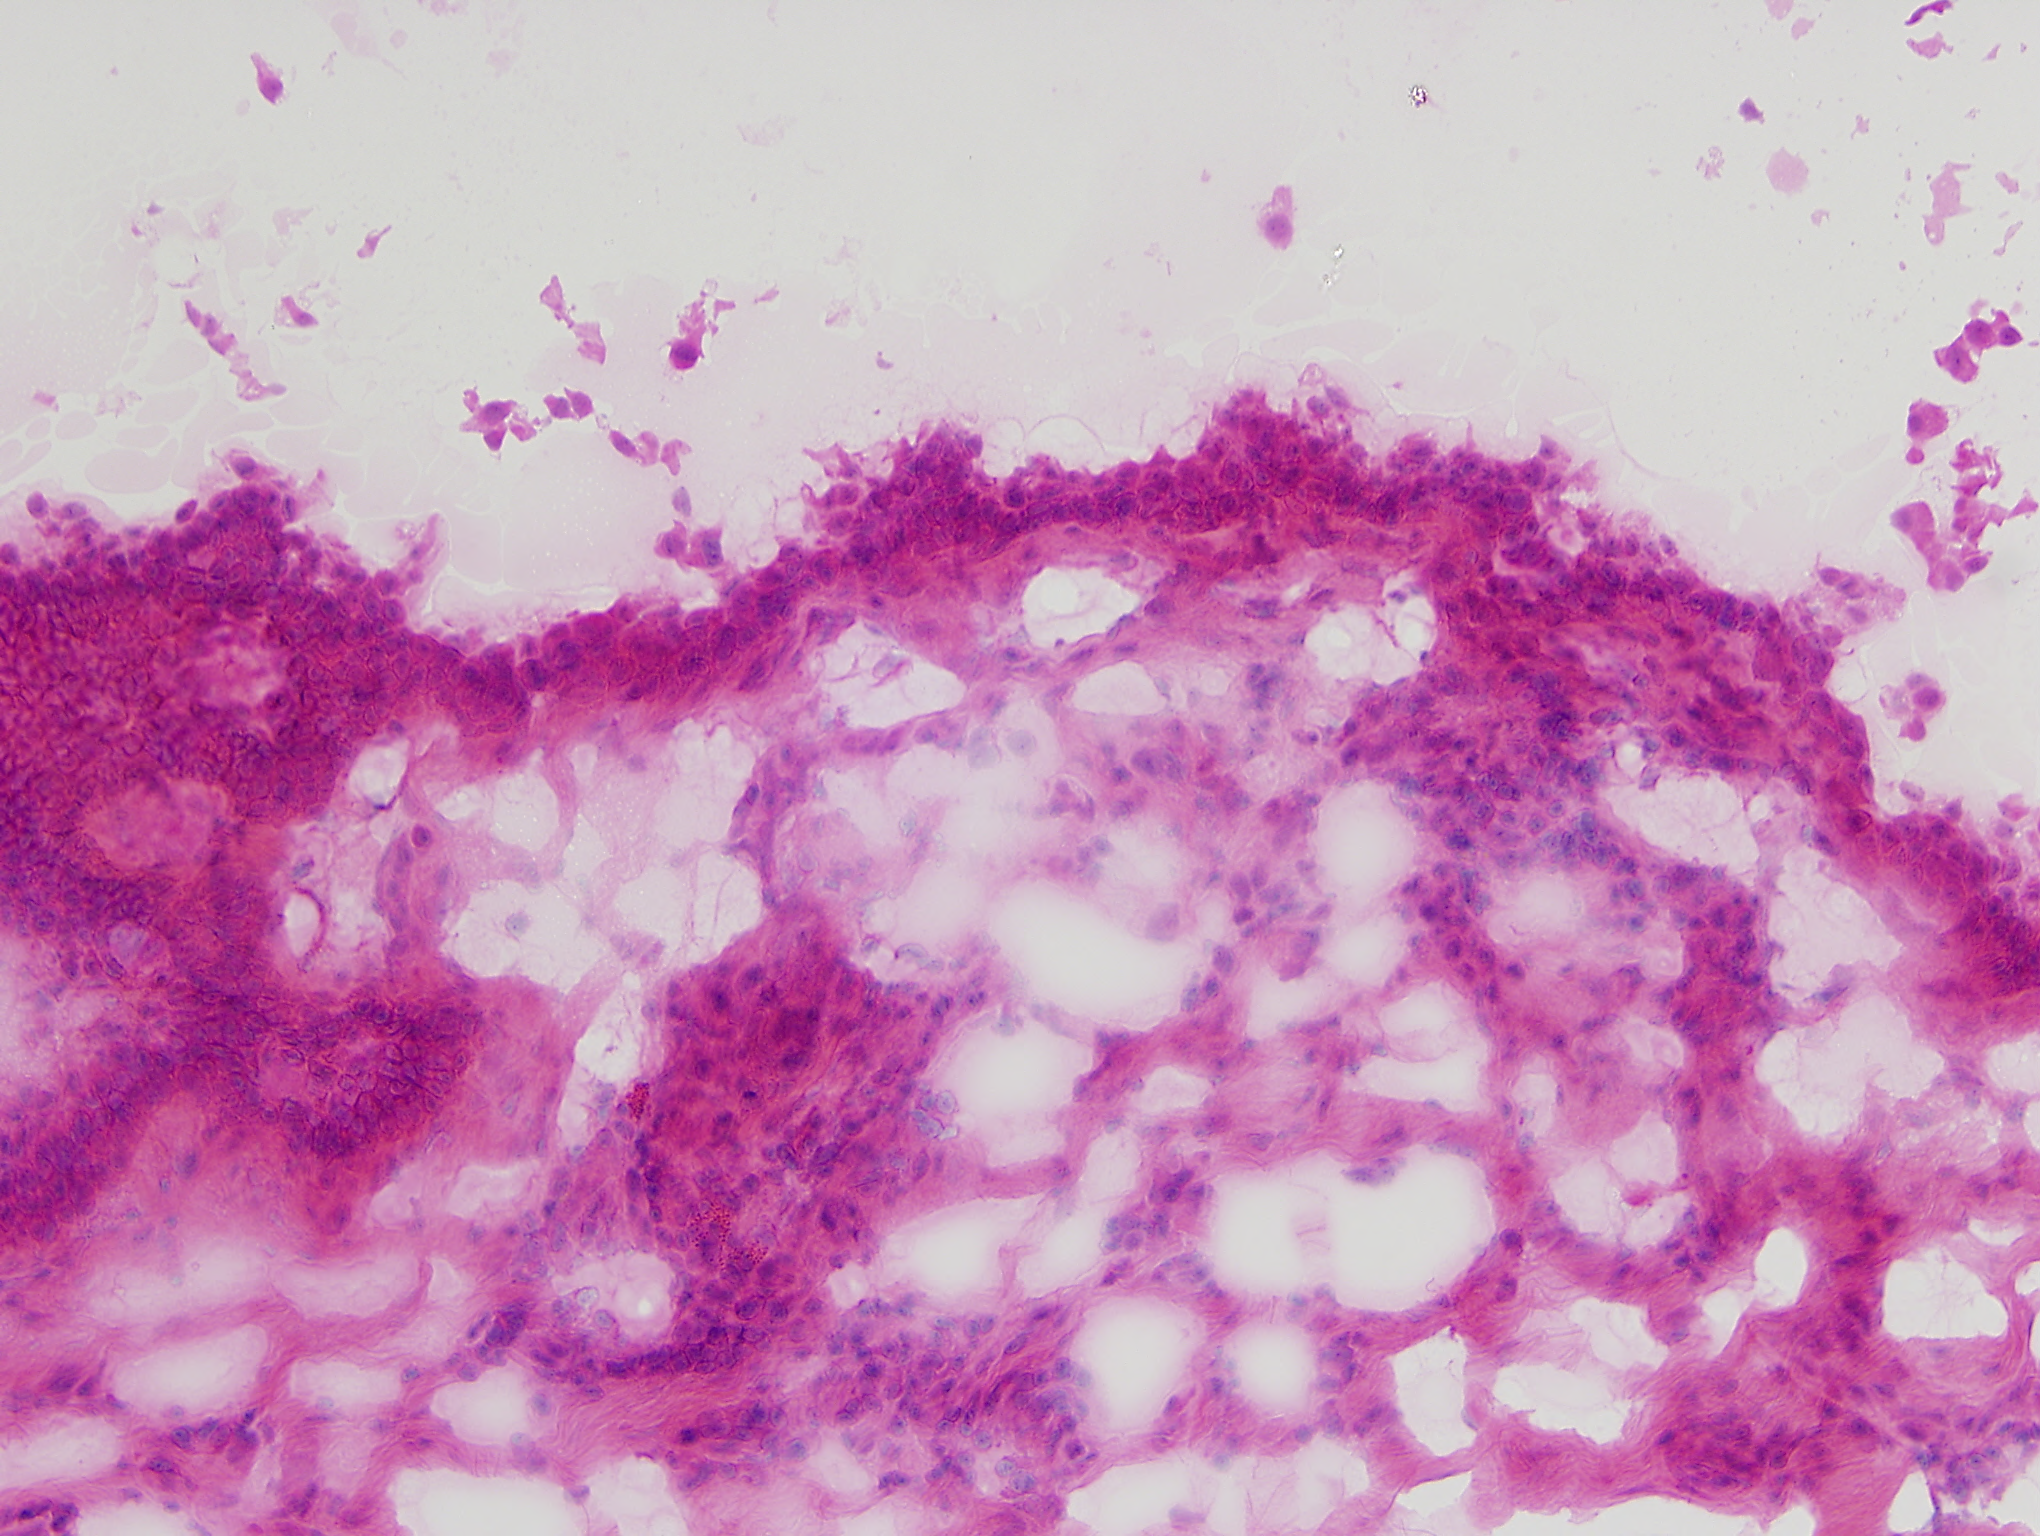
Single-field Hematoxylin and eosin (H&E) stained photomicrograph, about 1.0 x 0.8 mm across. Frozen section from the top of the tissue portion. Sample: solid tissue normal (non-tumour tissue), head and neck. Male patient; age at initial diagnosis 77 years.
- this section: solid tissue normal sample (biorepository sample class)
- patient diagnosis: Squamous cell carcinoma, NOS (larynx, NOS)